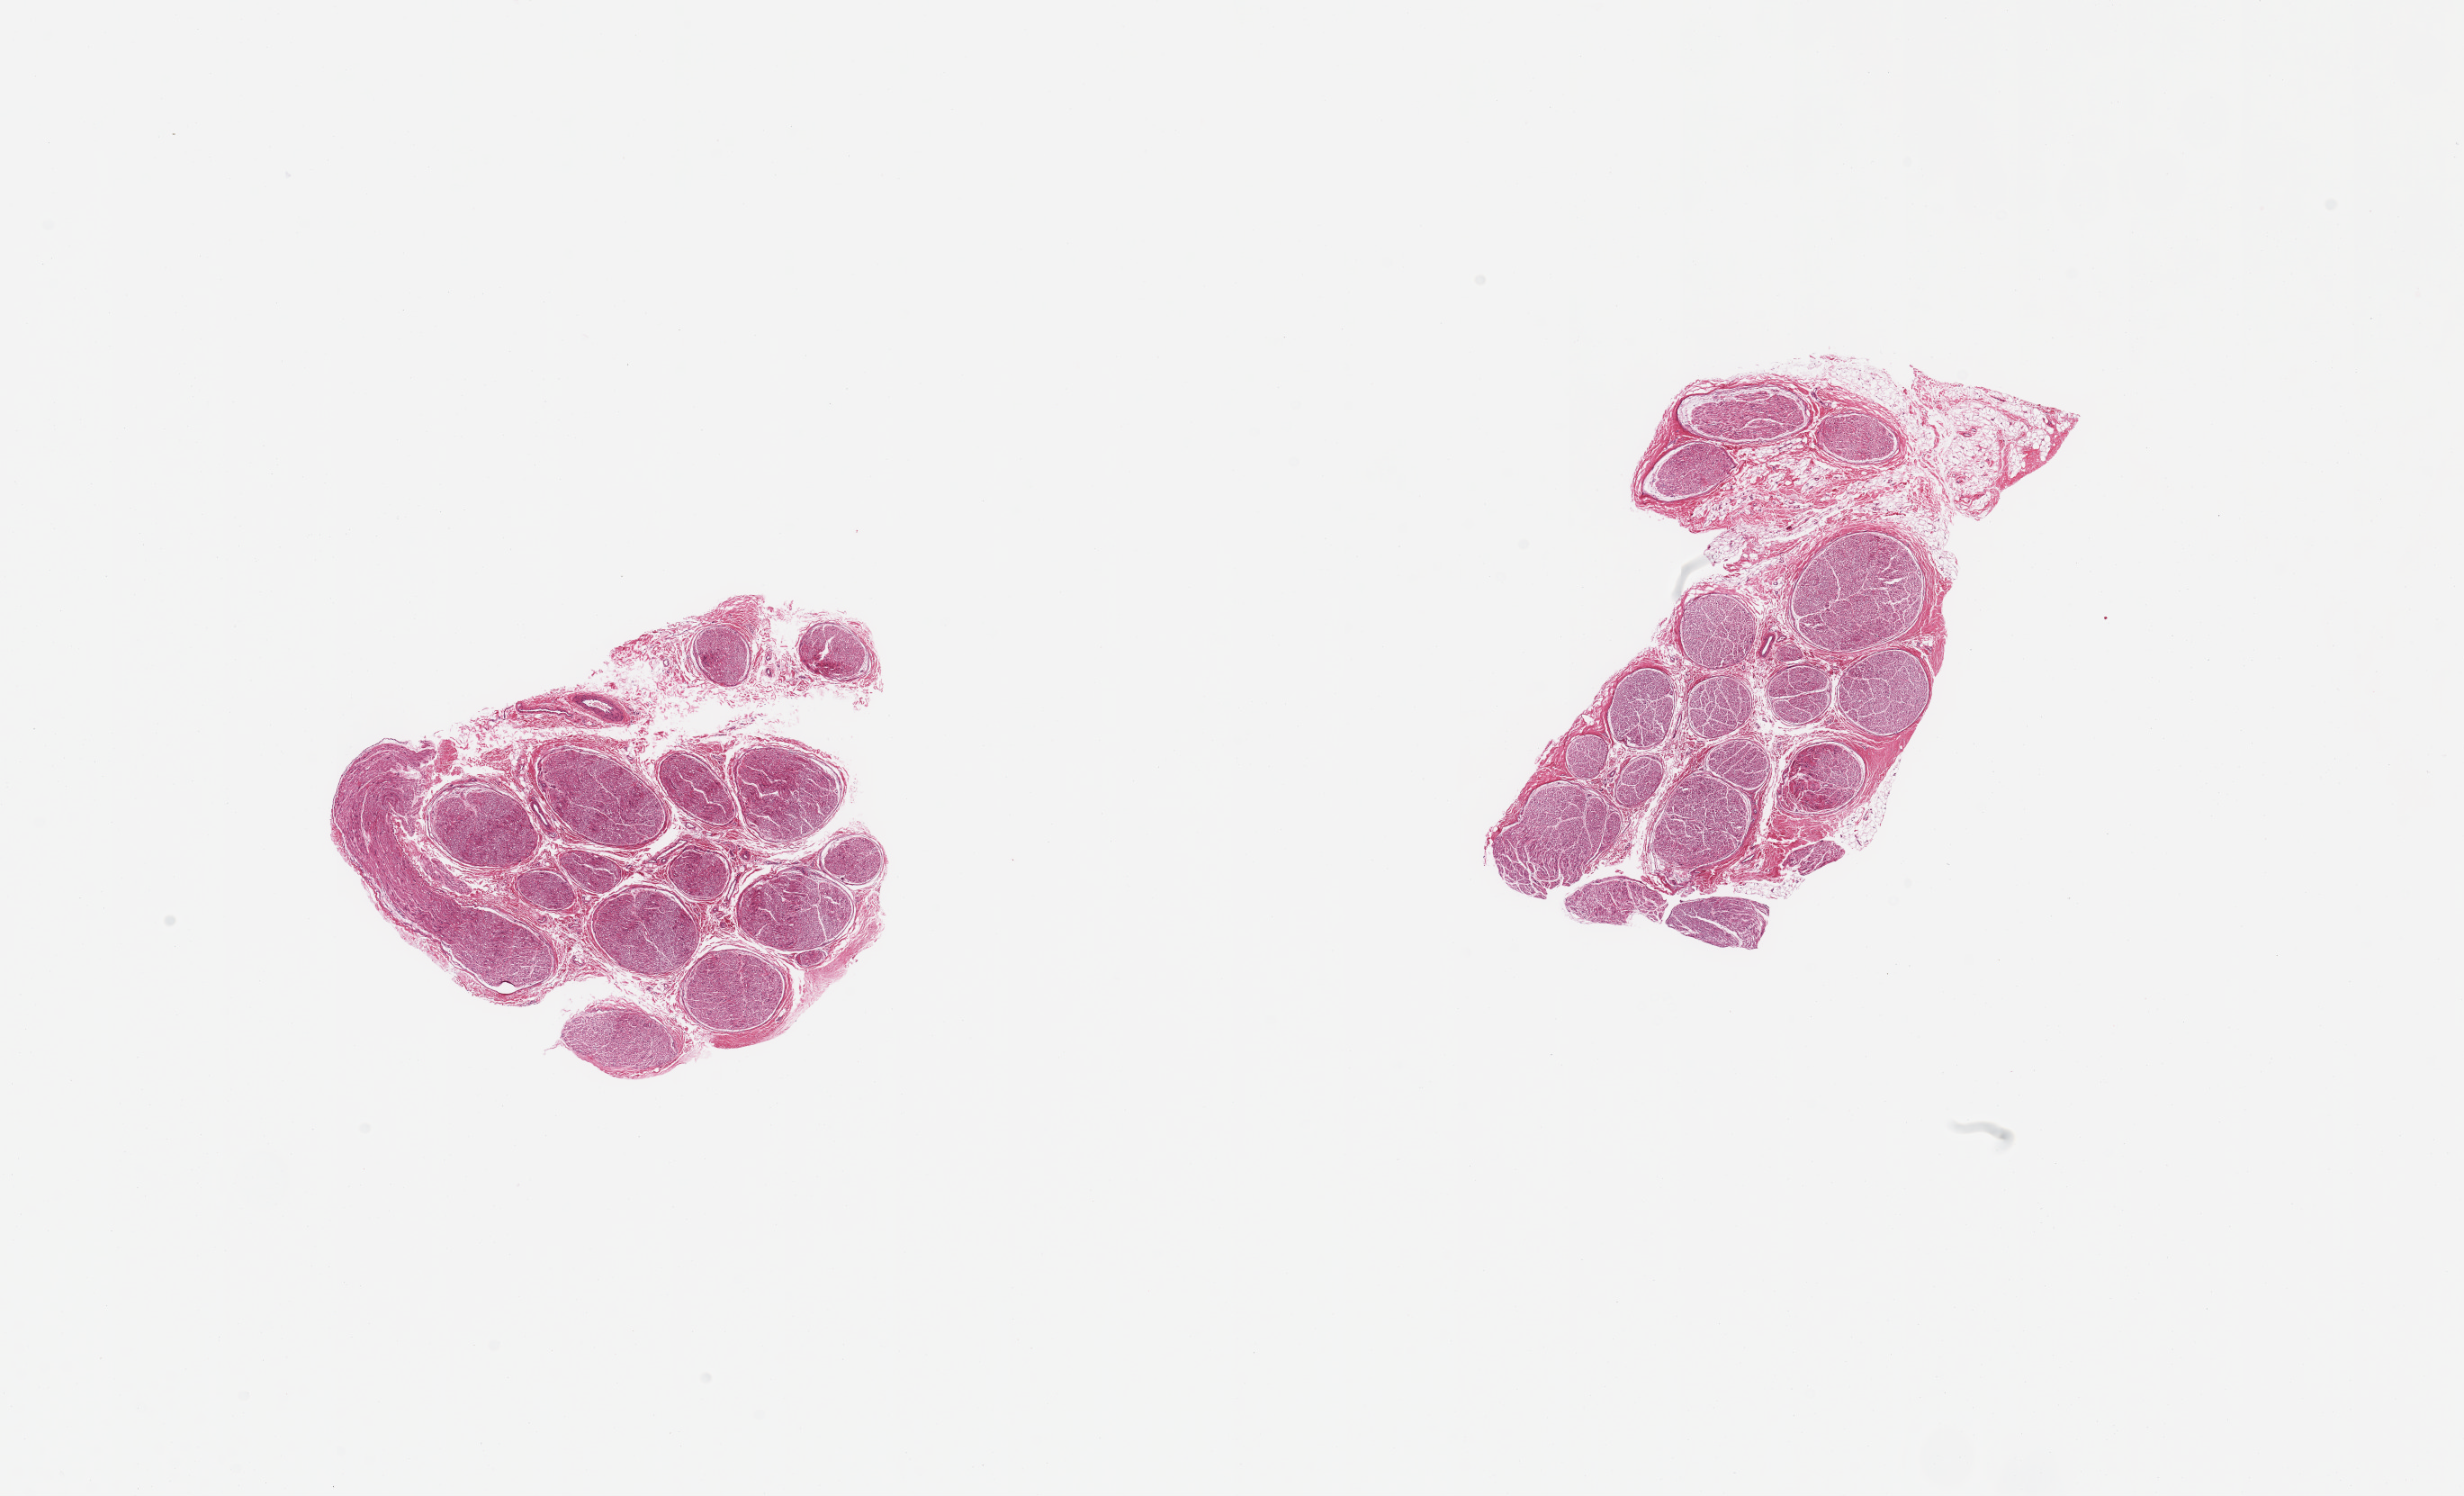
Digitized hematoxylin and eosin (H&E)-stained section, low-resolution overview of the scanned area, about 21.7 x 13.1 mm; PAXgene-fixed, paraffin-embedded tissue; section of tibial nerve (target tissue); donor tissue sample.
- review note (as recorded): 2 pieces, trace nubbin of adherent fat